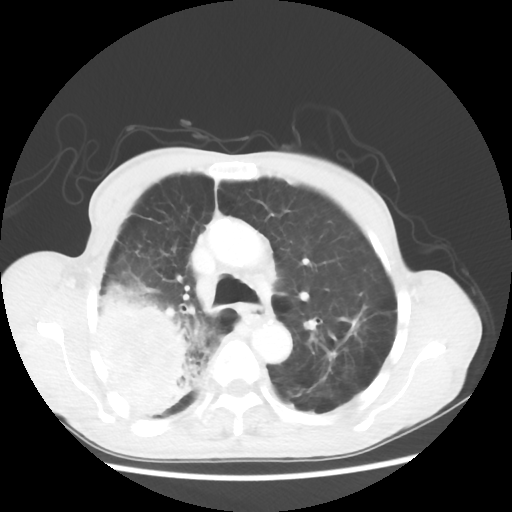
Chest CT, one axial slice; position 38 of 58 along the scan axis; reconstruction kernel STANDARD; 100 kVp; lung window (W 1500 / L -600 HU); 5 mm slice thickness; 512 × 512 image matrix. Male patient, age 75 years. From the clinical record (not read from this slice): clinical TNM (as recorded): T4 N1 M1.
Structures marked on this image (rectangle marked by the reading radiologist):
- lung tumour (recorded histology: adenocarcinoma): bounding box <91,275,208,418> (left, top, right, bottom; pixels)